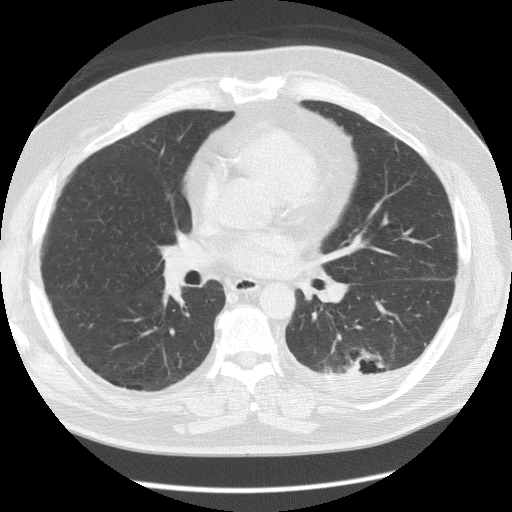
Chest CT (low-dose screening protocol), one axial image, baseline annual screen, lung window (W 1500 / L -600 HU), 2.5 mm slice thickness, slice 60 of 126 in the series. Male, age 56 years at enrolment.
Expert-annotated lung lesion, bounding box [x1, y1, x2, y2] px = [324, 342, 396, 394]. The screening reader recorded 4 non-calcified nodules or masses ≥4 mm on this exam (left lower lobe, left lower lobe, right middle lobe, left upper lobe); which of them this box marks is not recorded. Official screen result: positive, change unspecified: nodule(s) >= 4 mm or enlarging nodule(s), mass(es), or other non-specific abnormalities suspicious for lung cancer.